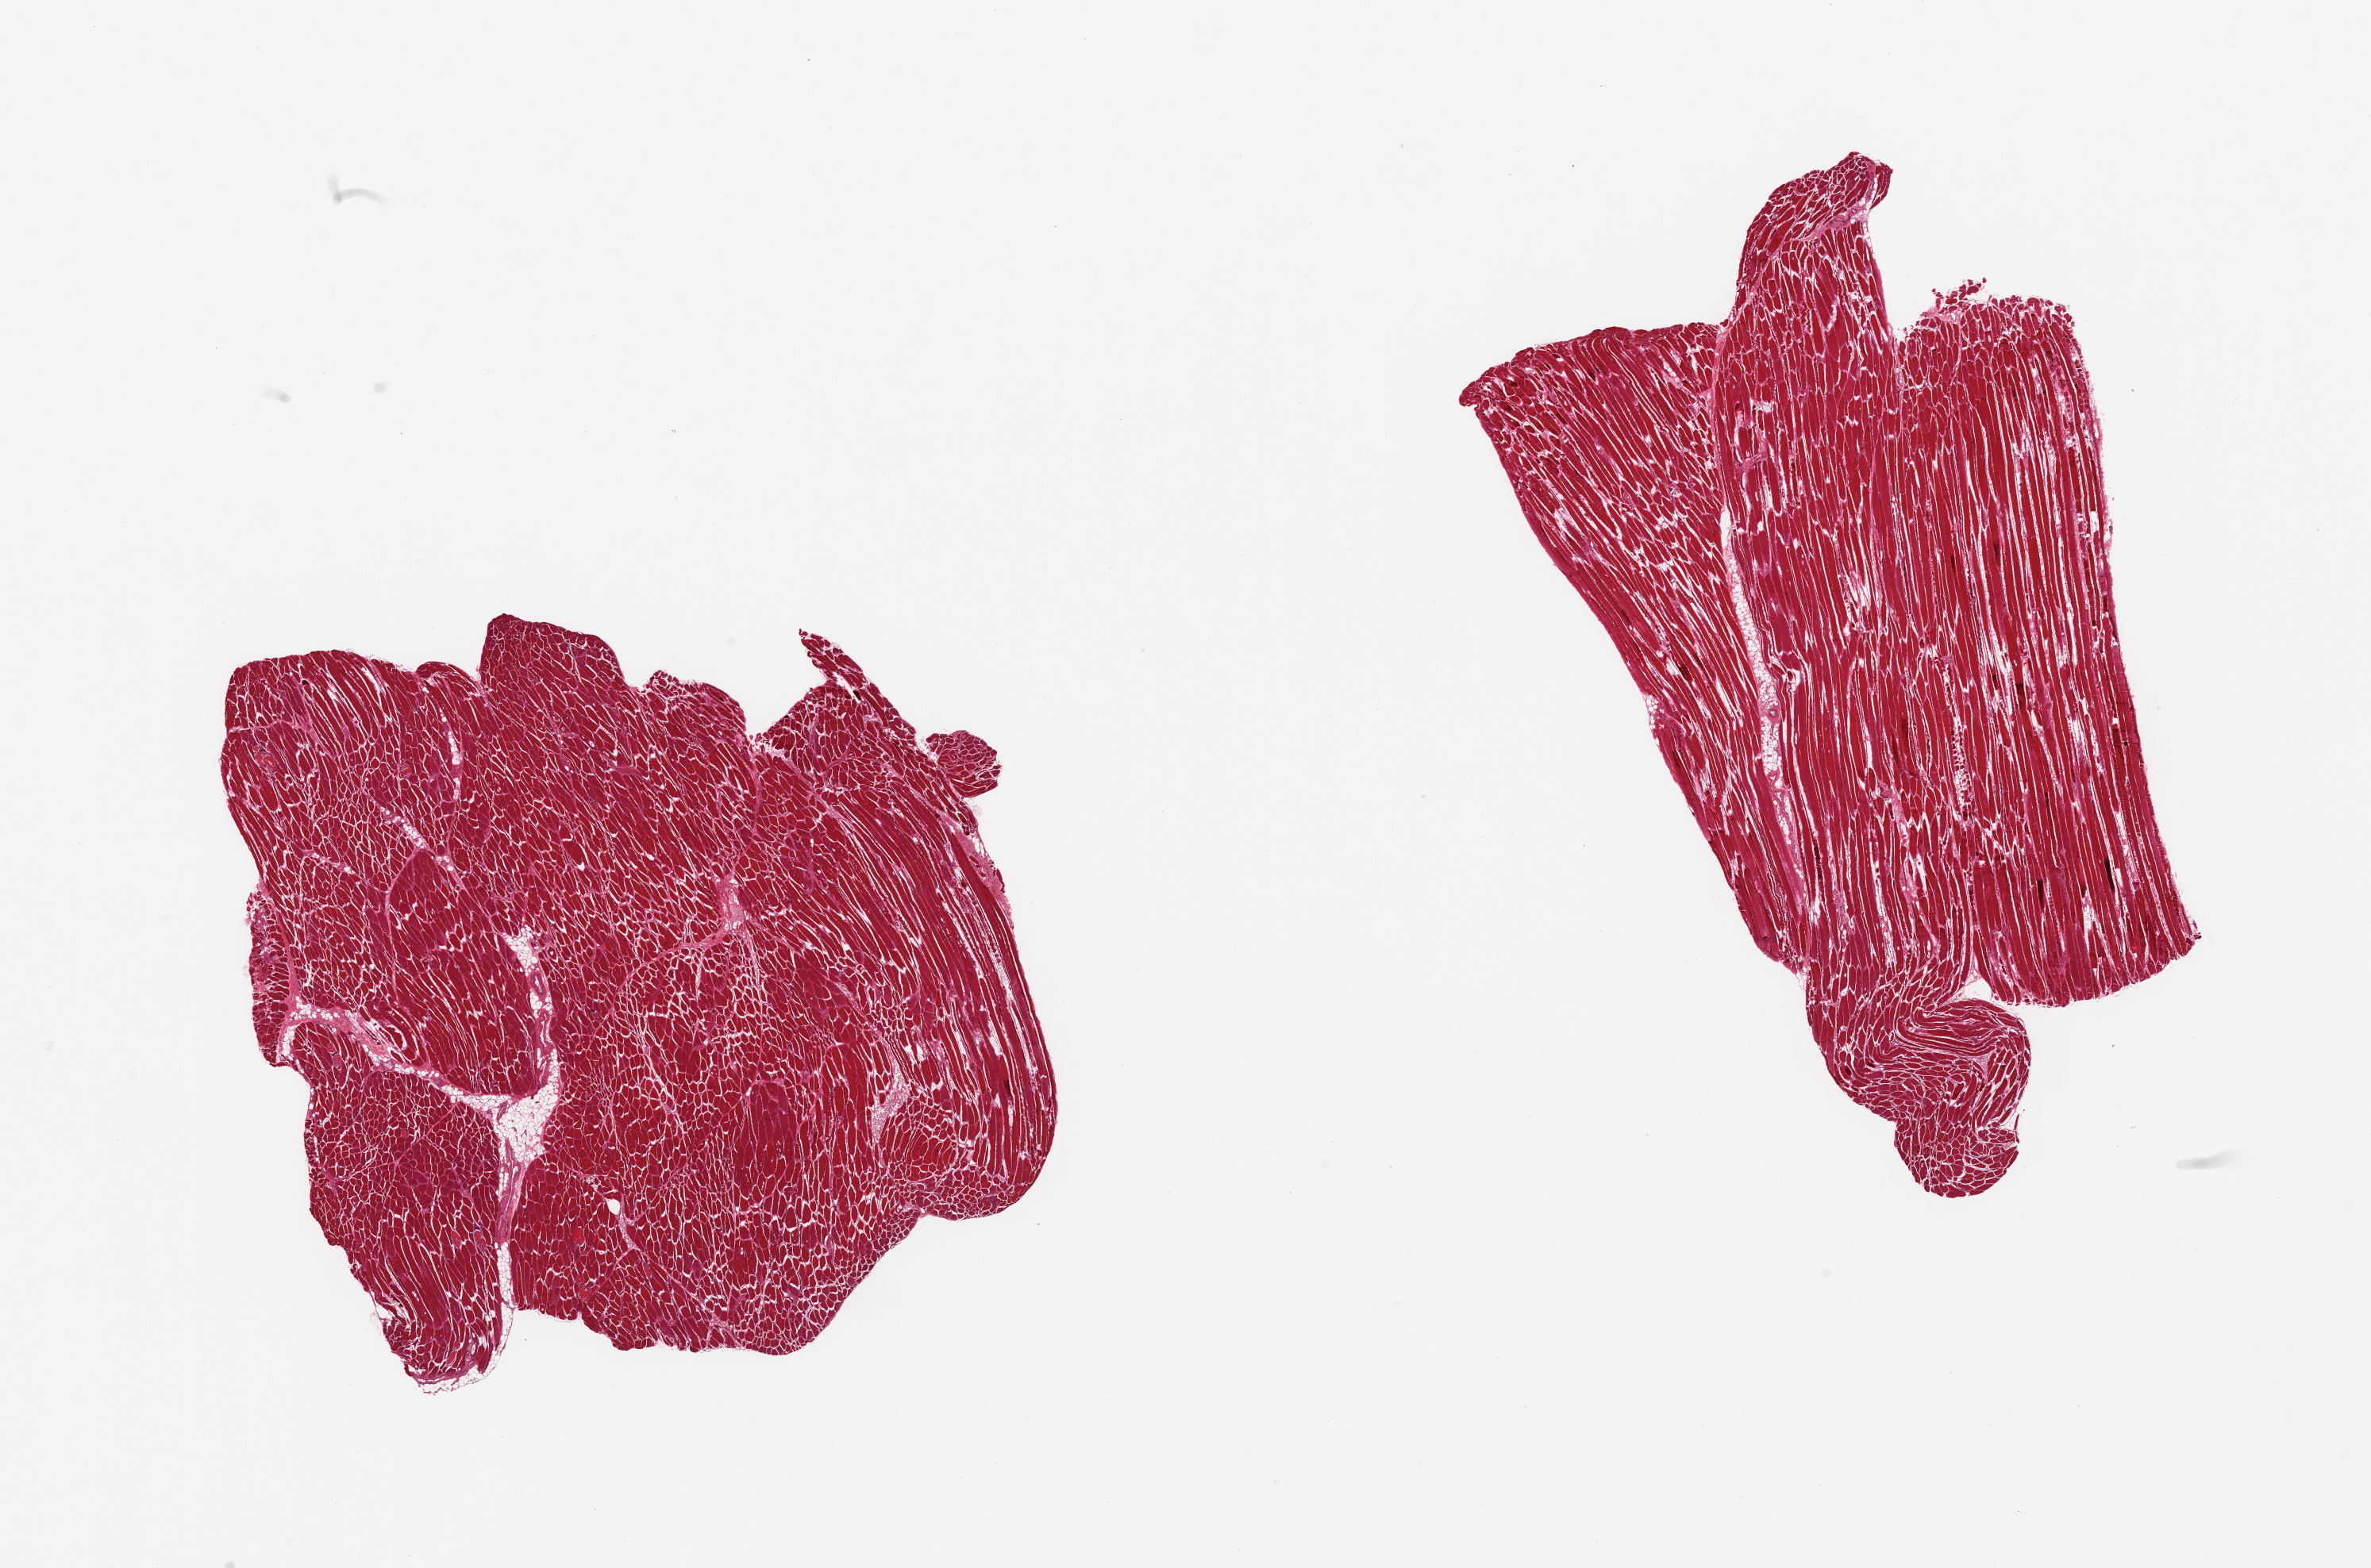
Digitized hematoxylin and eosin (H&E)-stained section, brightfield — a low-resolution overview of the entire scanned area, about 23.6 x 15.6 mm, PAXgene-fixed, paraffin-embedded tissue, target tissue: skeletal muscle, tissue donor sample. Donor sex: female.
Pathologist's review note for this sample: 2 pieces.